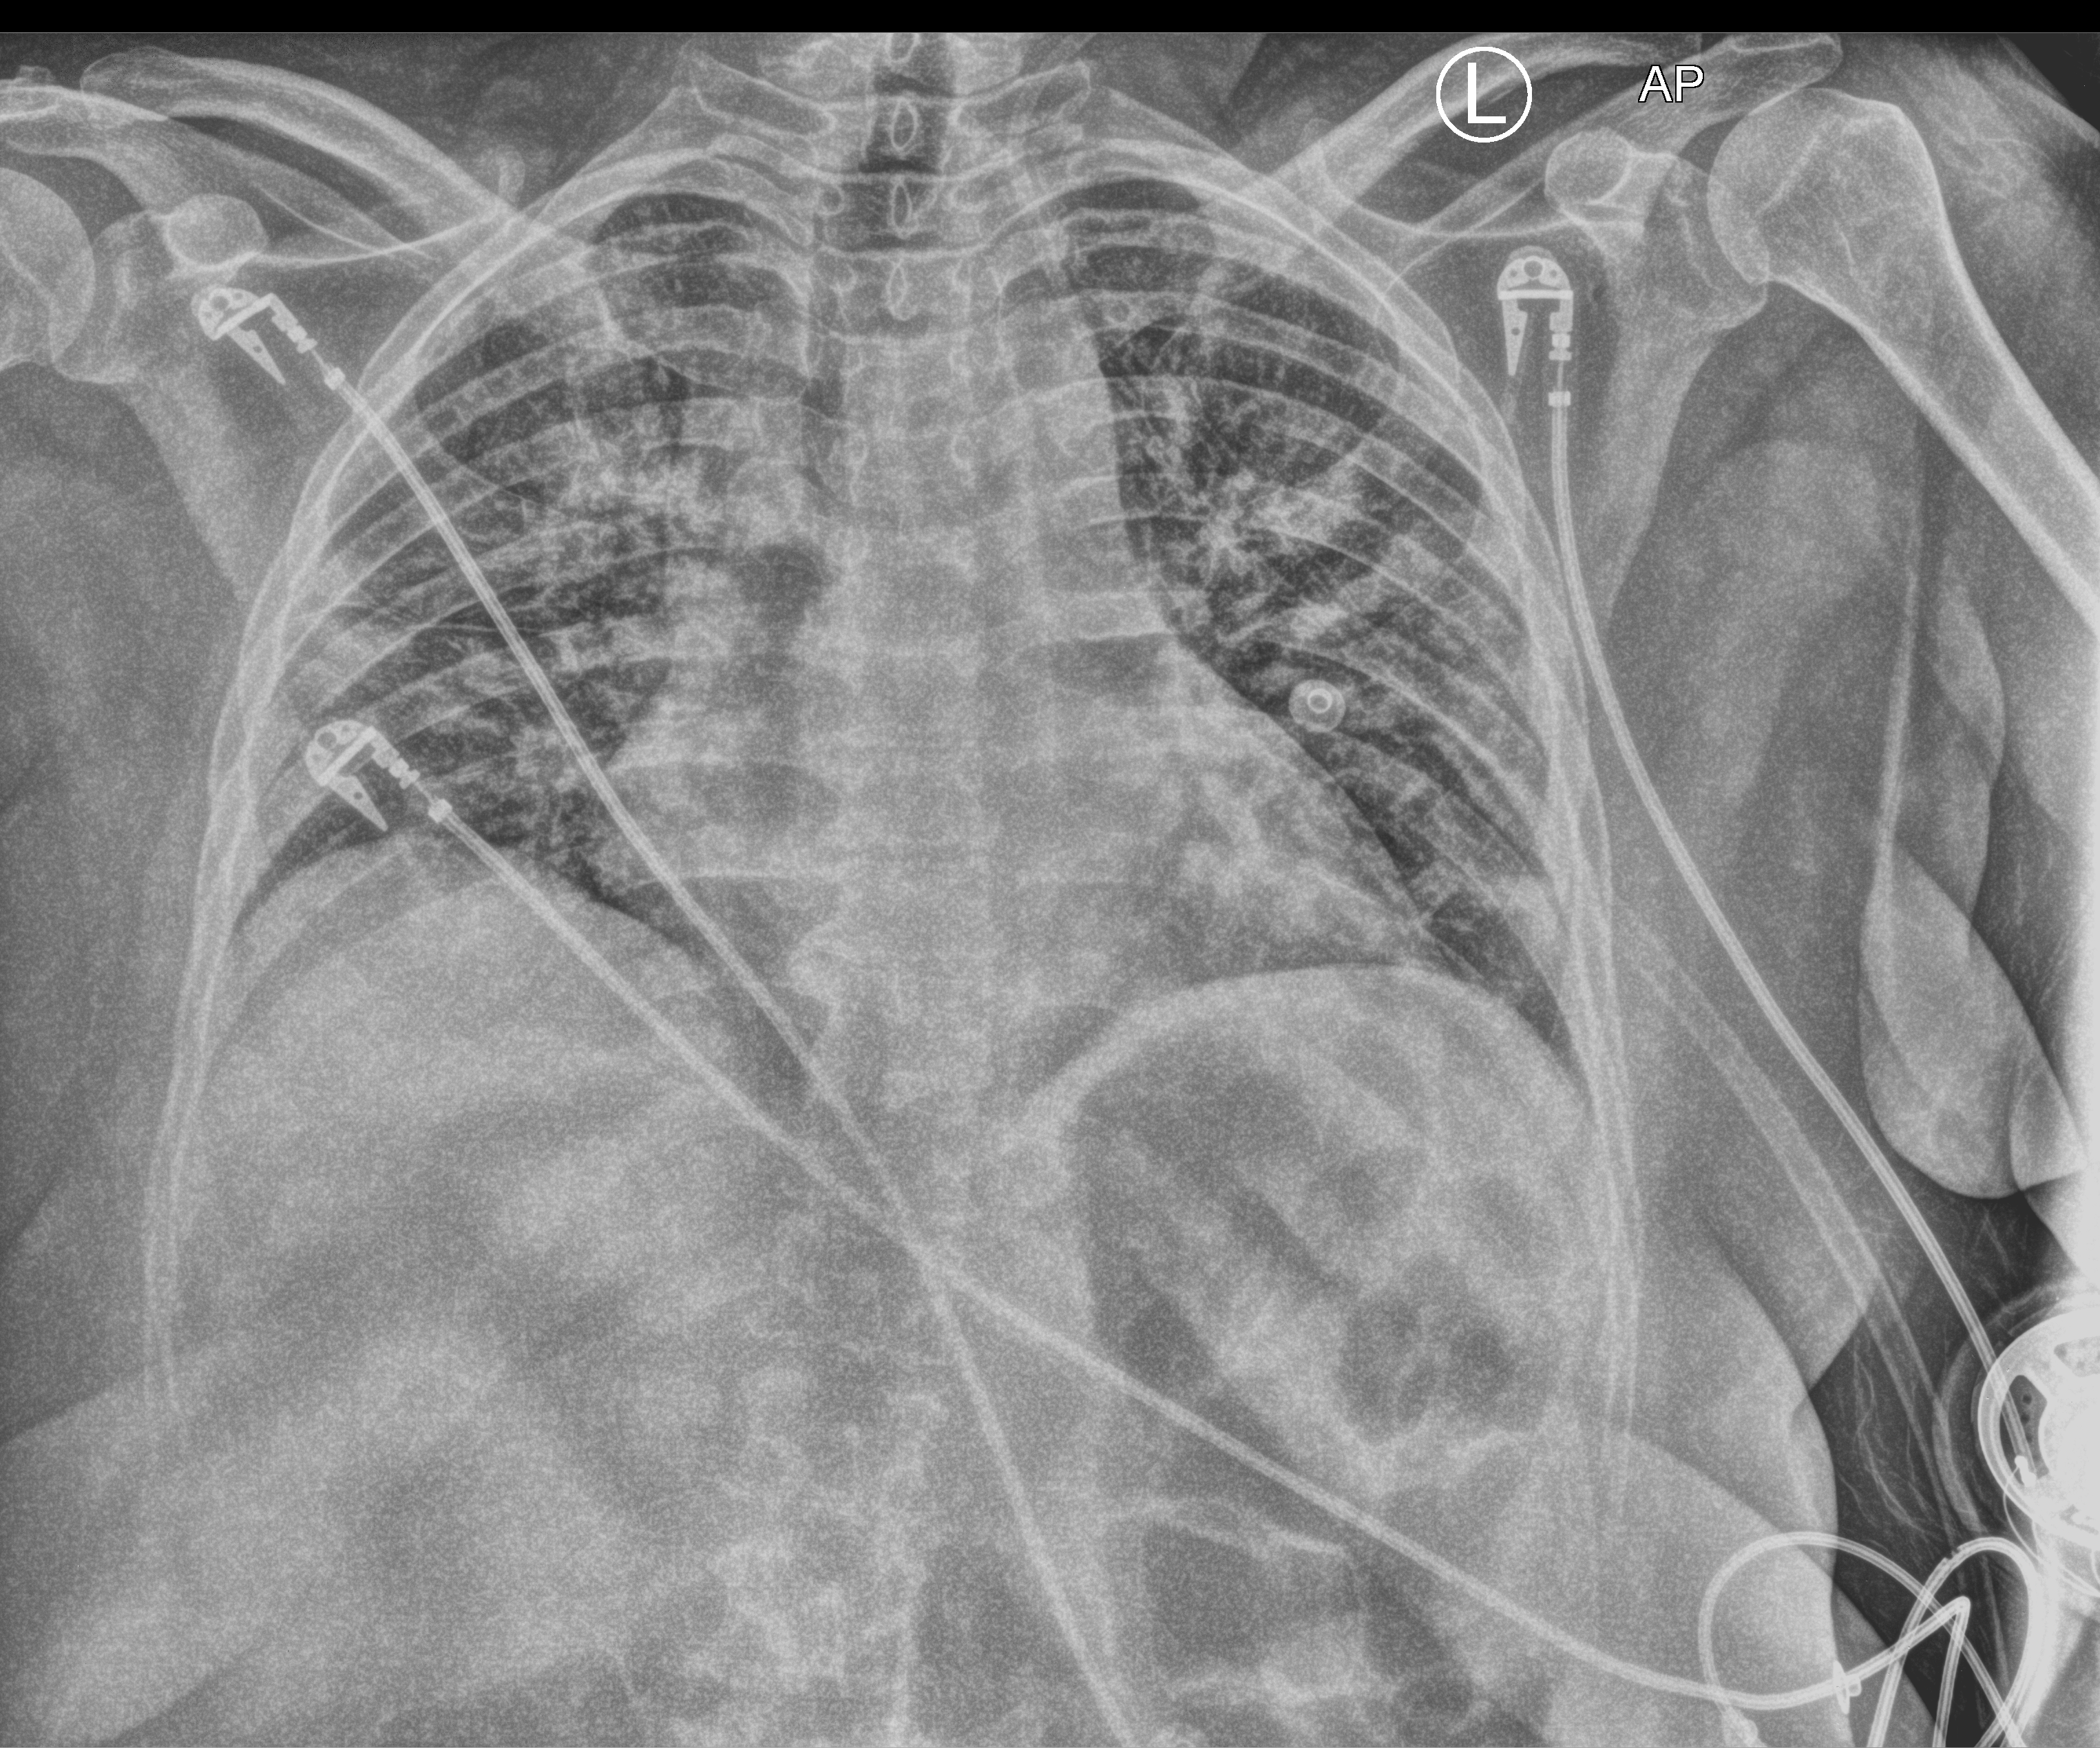
Portable chest radiograph; anteroposterior (AP) projection. Female patient hospitalised with COVID-19, age 18–59 years.
Hospital-stay facts (about this admission, not read from this image; timing relative to this image not recorded):
- length of hospital stay: 6 days
- admitted to intensive care during this hospital stay: yes
- mechanically ventilated during this hospital stay: no